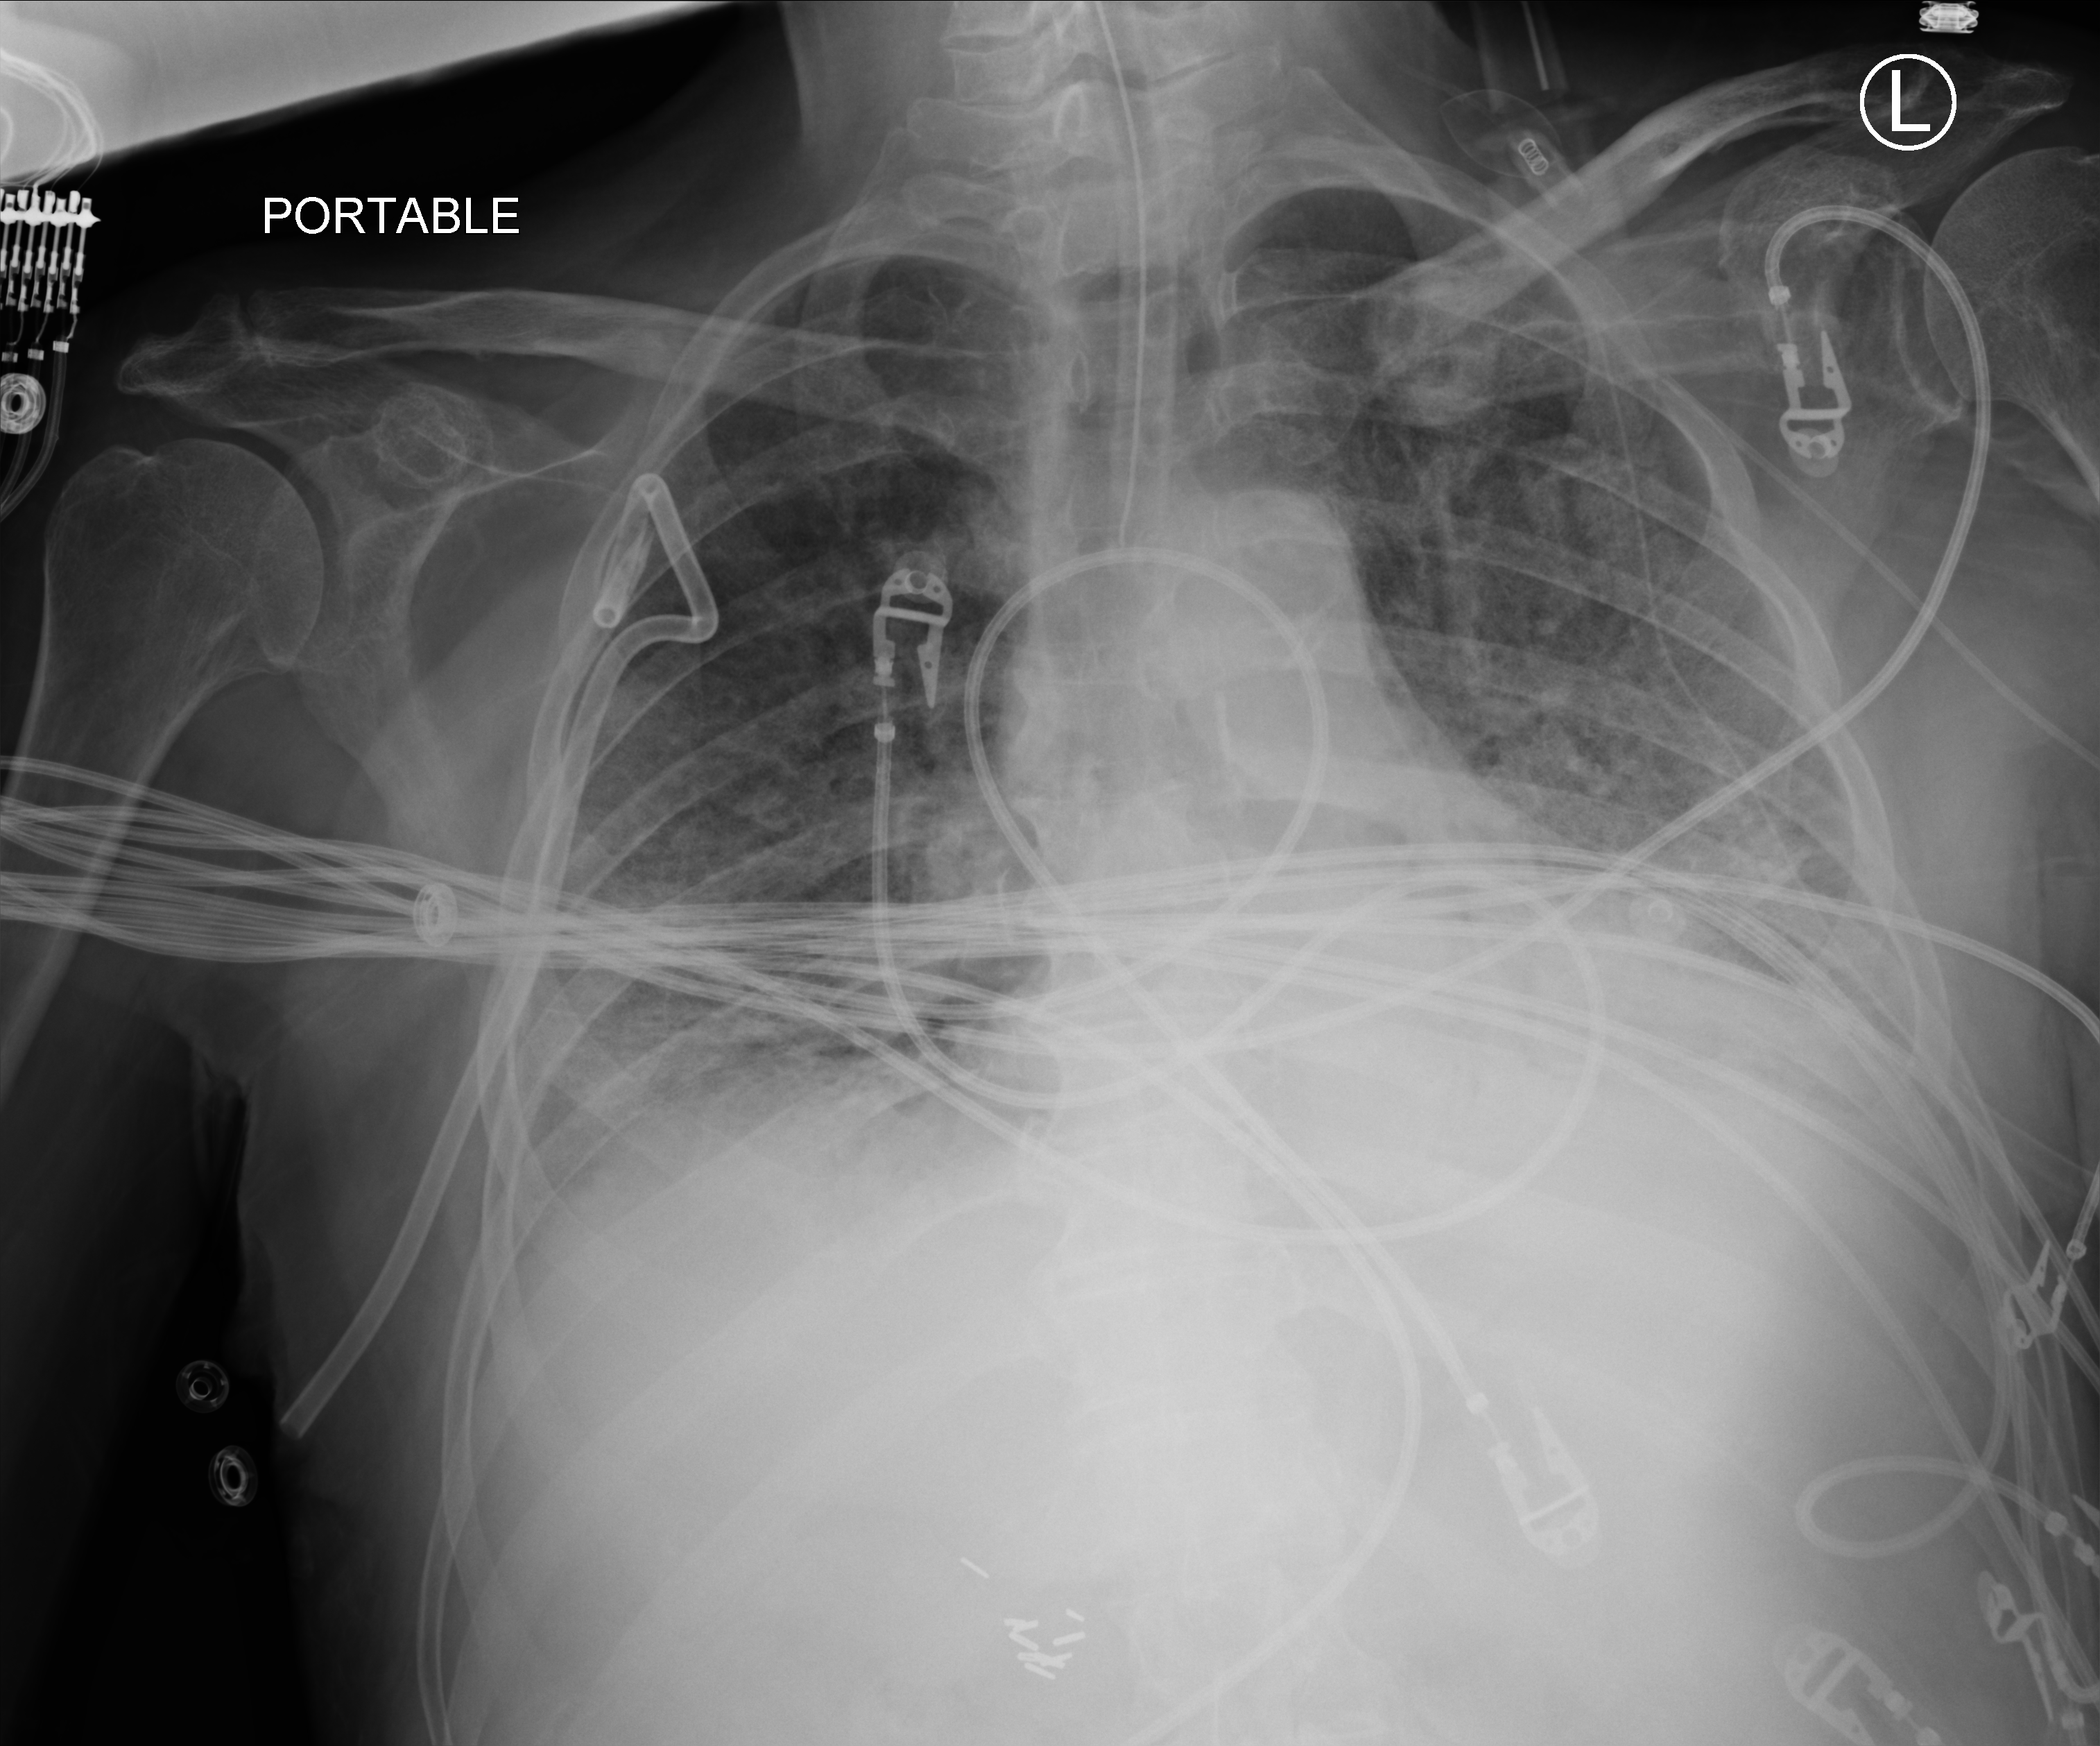
Bedside chest radiograph (computed radiography). Patient hospitalised with COVID-19; male, aged 75–90 years.
Hospital-stay facts (about this admission, not read from this image; timing relative to this image not recorded): smoking status (admission record): never; length of hospital stay: 23 days; mechanically ventilated during this hospital stay: yes.